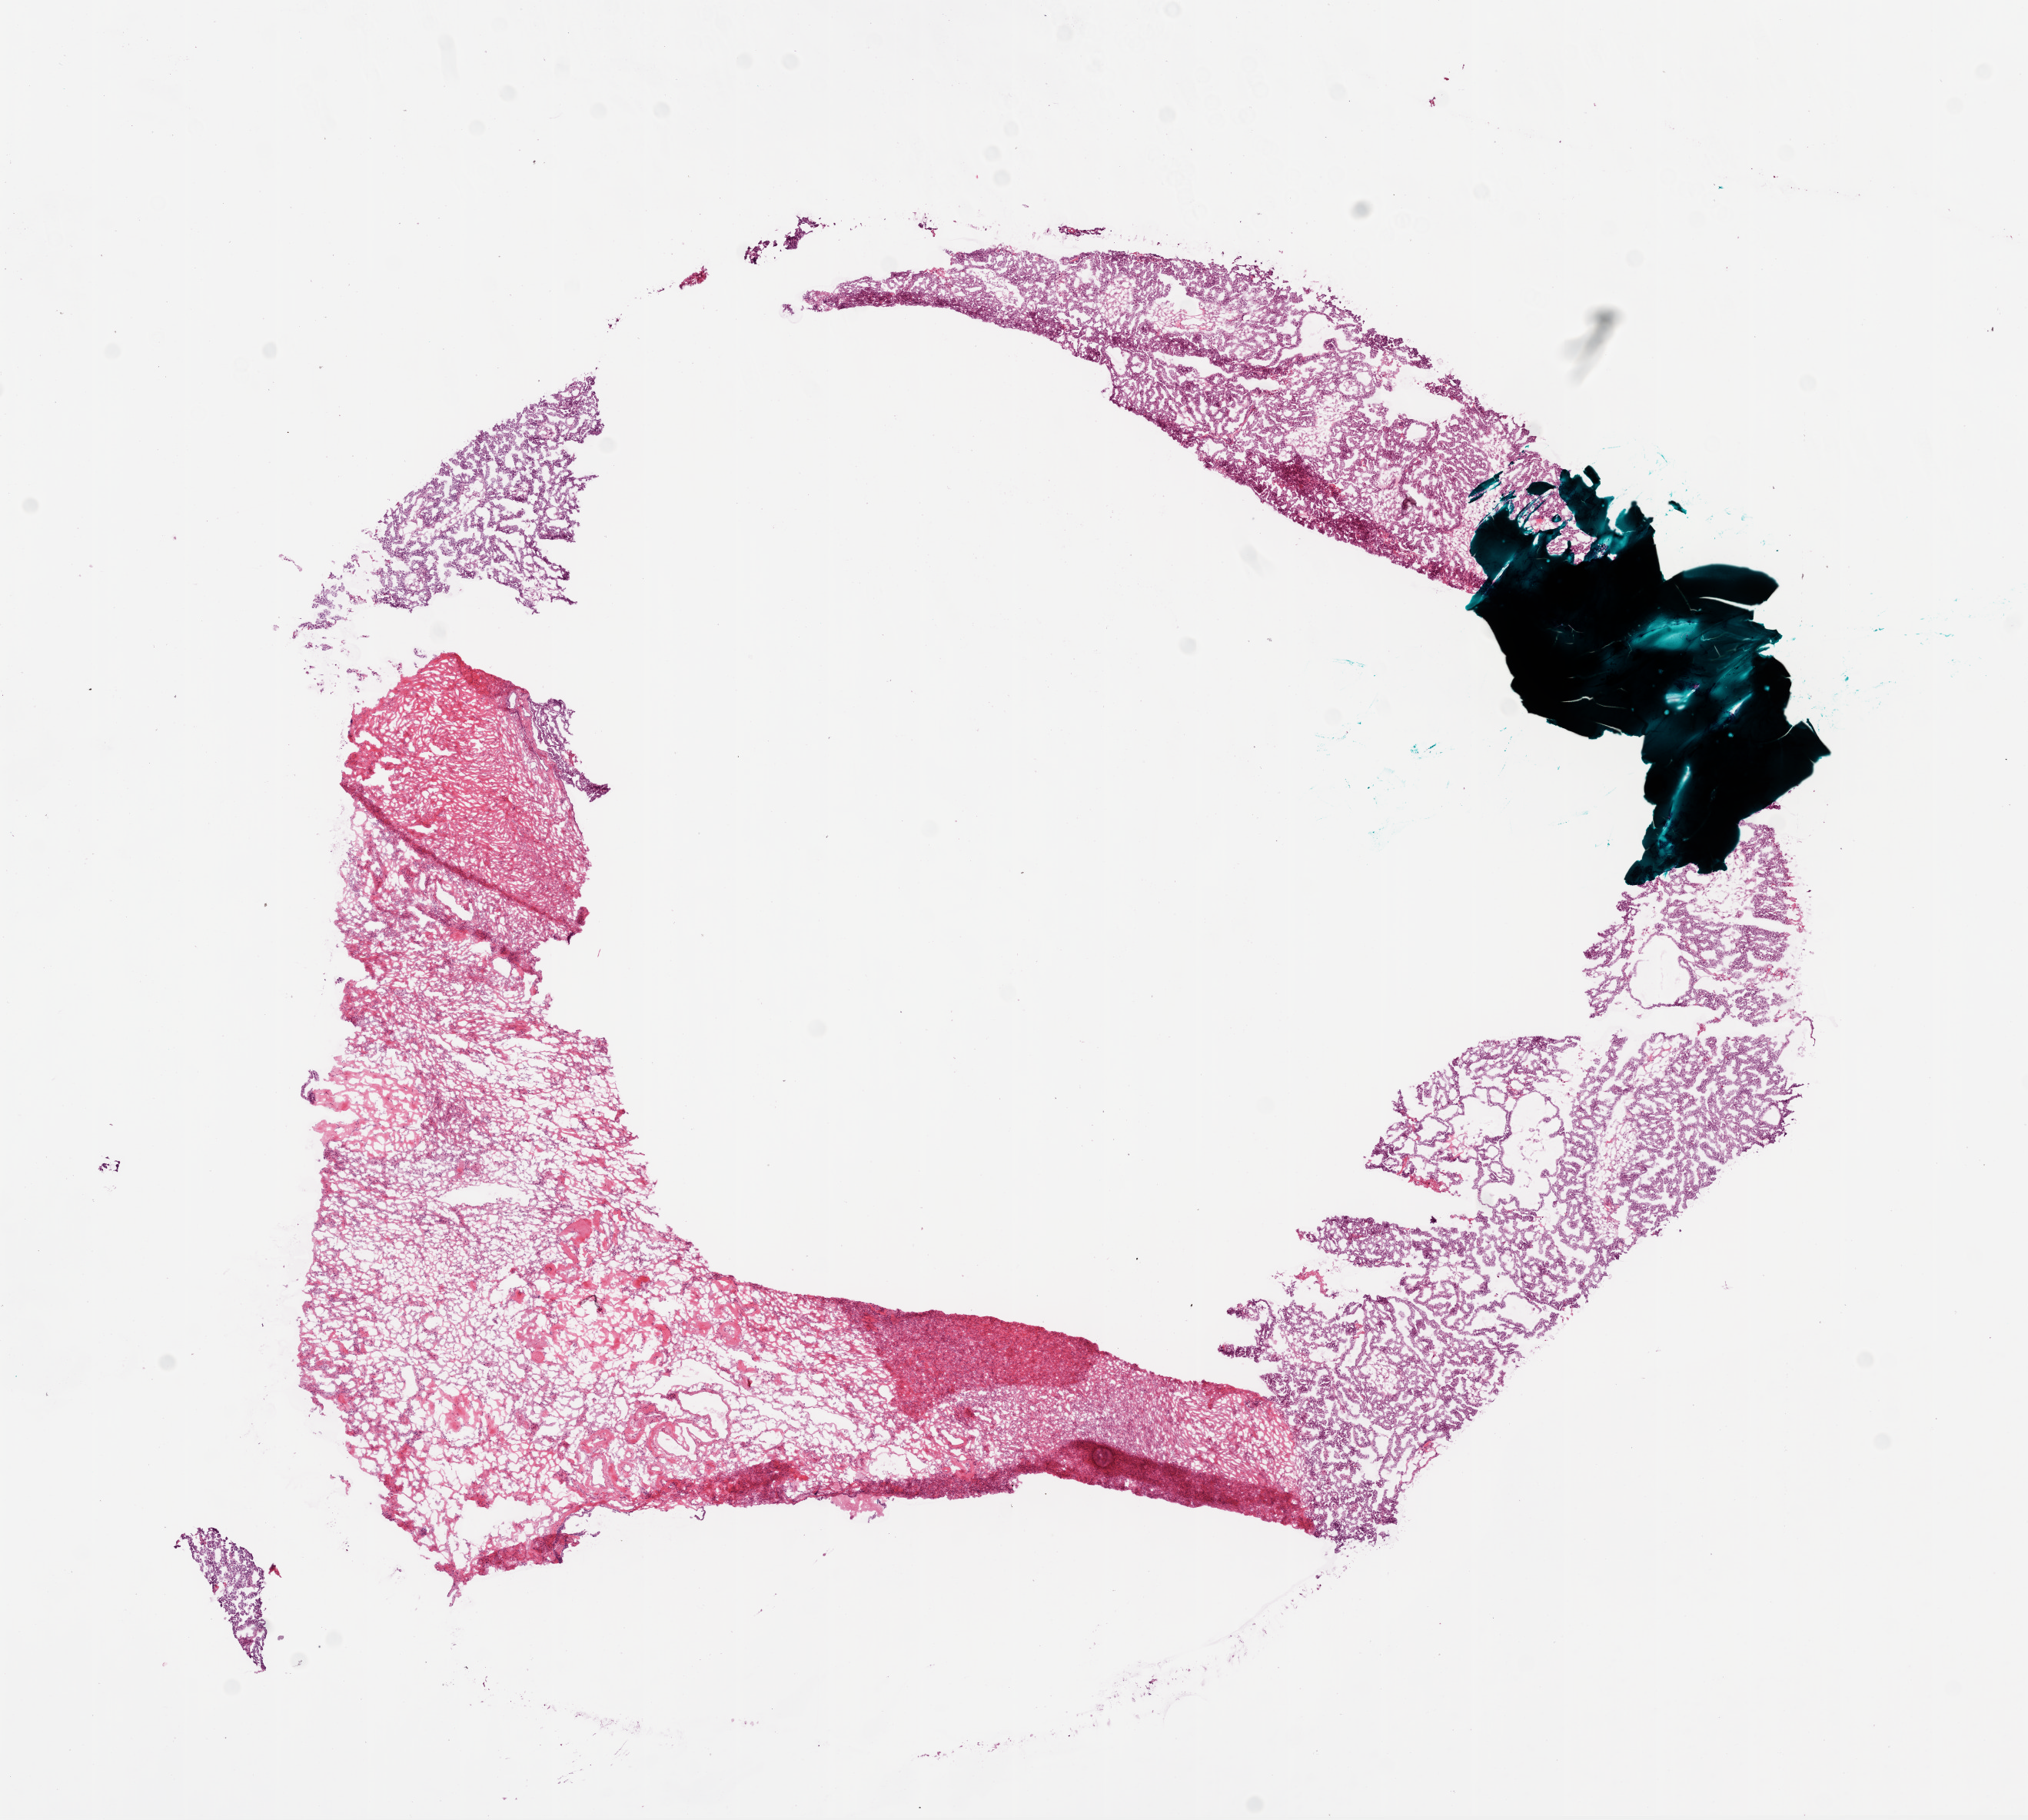
Digitized H&E tissue section (whole slide) — a low-resolution overview of the entire scanned area, about 10.6 x 9.5 mm (acquisition: 20x scan), frozen section from the bottom of the tissue portion, sample: primary tumour, ovary. Female, age 67 years at initial diagnosis.
Histologic diagnosis: Serous cystadenocarcinoma, NOS.